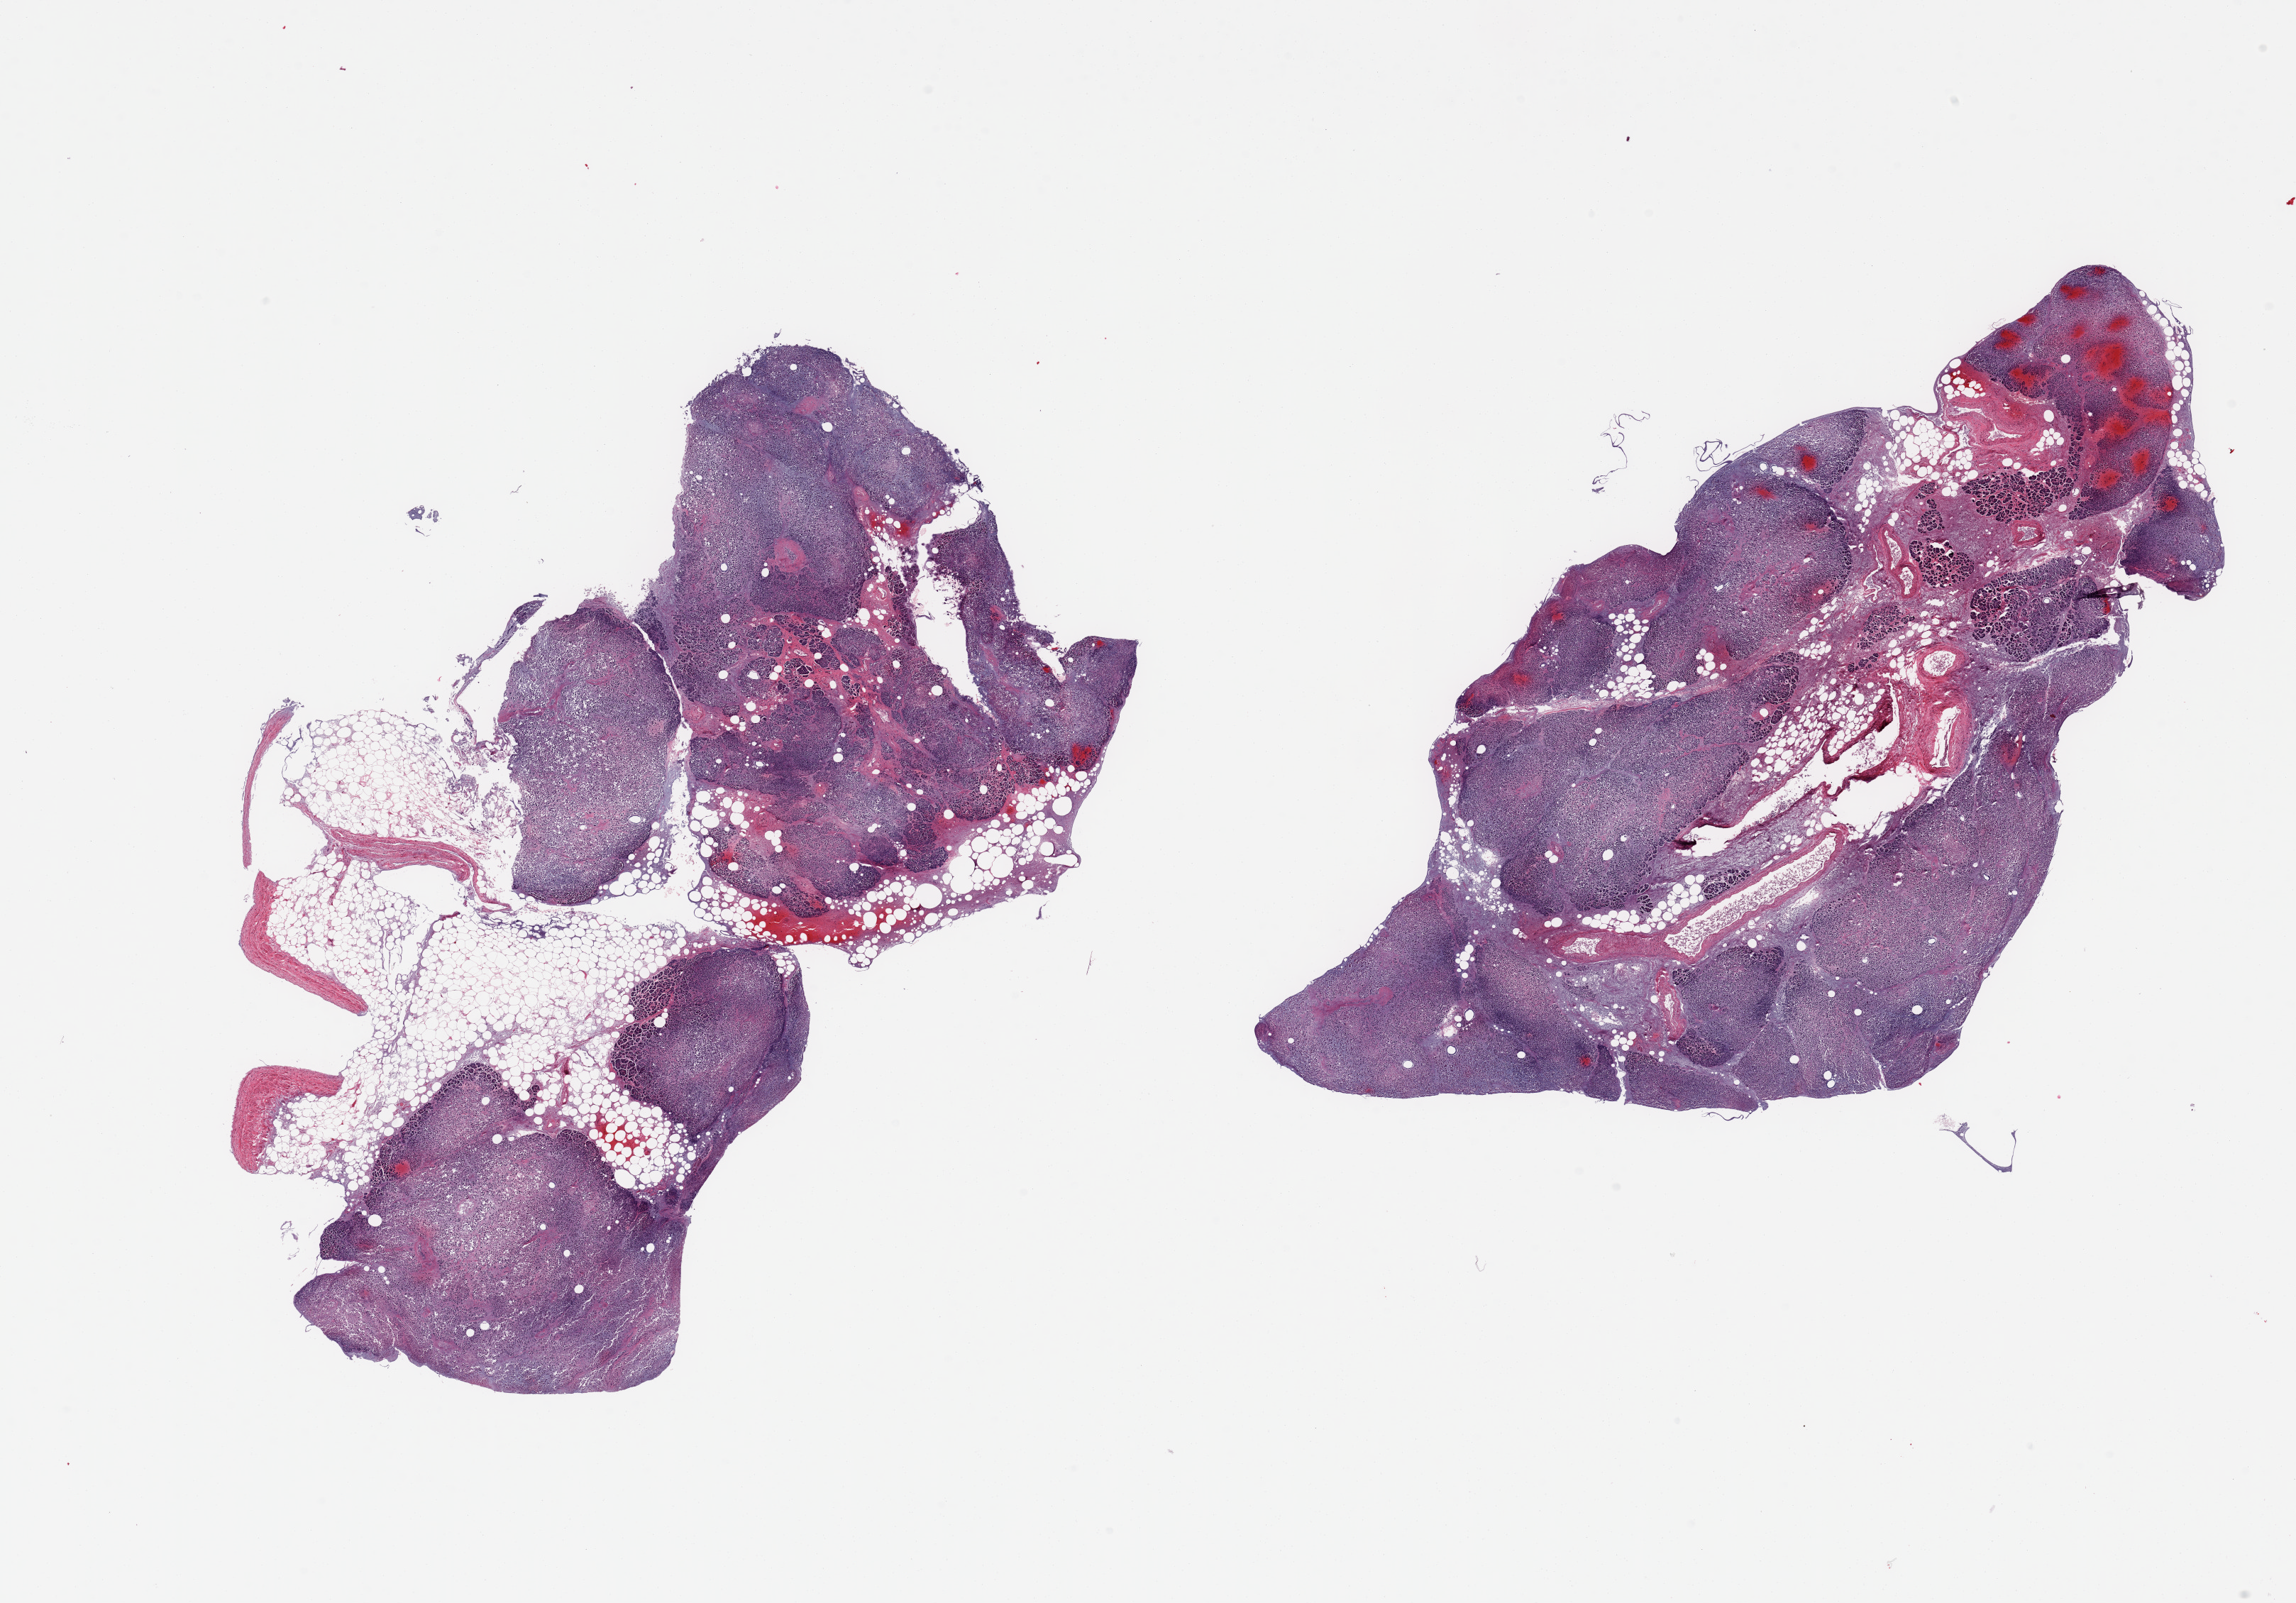
Hematoxylin and eosin (H&E) whole-slide image, brightfield, a low-resolution overview of the entire scanned area, about 25.6 x 17.9 mm, PAXgene-fixed paraffin-embedded (PFPE) section, section of pancreas (target tissue), tissue donor sample. Male donor.
Review note (as recorded): 2 pieces, advanced saponification, Islets degraded.